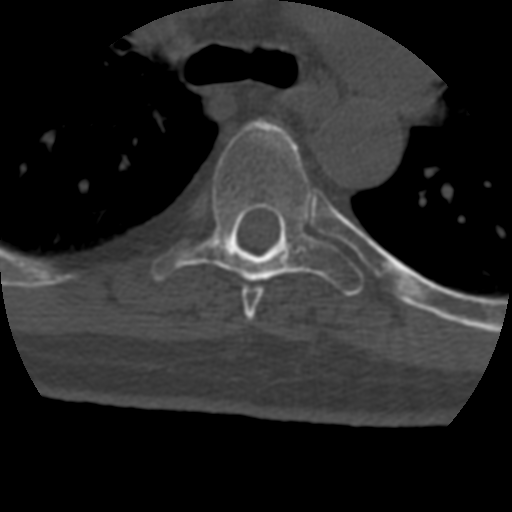
CT including the spine, one axial slice; 120 kVp; bone window (W 1800 / L 400 HU); 512 × 512 image matrix. Patient age 69 years. From the clinical record (not read from this slice): primary cancer: prostate.
Outlined on this slice (semi-automatically segmented with operator editing):
- T5 vertebra: bounding box [x1, y1, x2, y2] px = [242, 128, 296, 322]
- T6 vertebra: [152, 120, 364, 296]